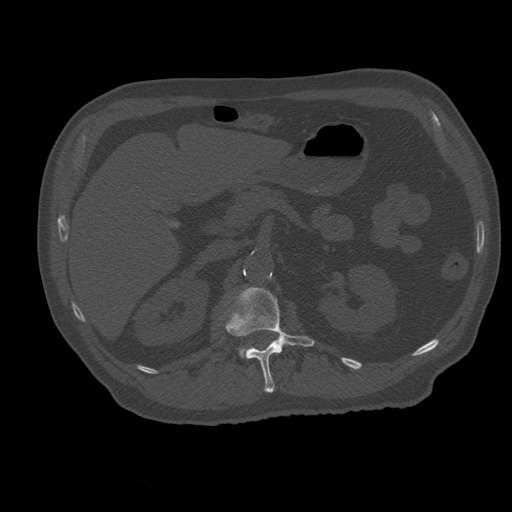
CT including the spine, one axial slice. Reconstruction kernel STANDARD. 120 kVp. Bone window (W 1800 / L 400 HU). 512 × 512 image matrix, field of view 407 × 407 mm. Patient age 73 years. Case-level facts recorded for this patient, not image findings: primary cancer: prostate.
Outlined on this slice (semi-automatically segmented with operator editing):
- L1 vertebra: bounding box (x1, y1, x2, y2) in pixels: (226, 287, 315, 393)
- L2 vertebra: (239, 349, 246, 357)